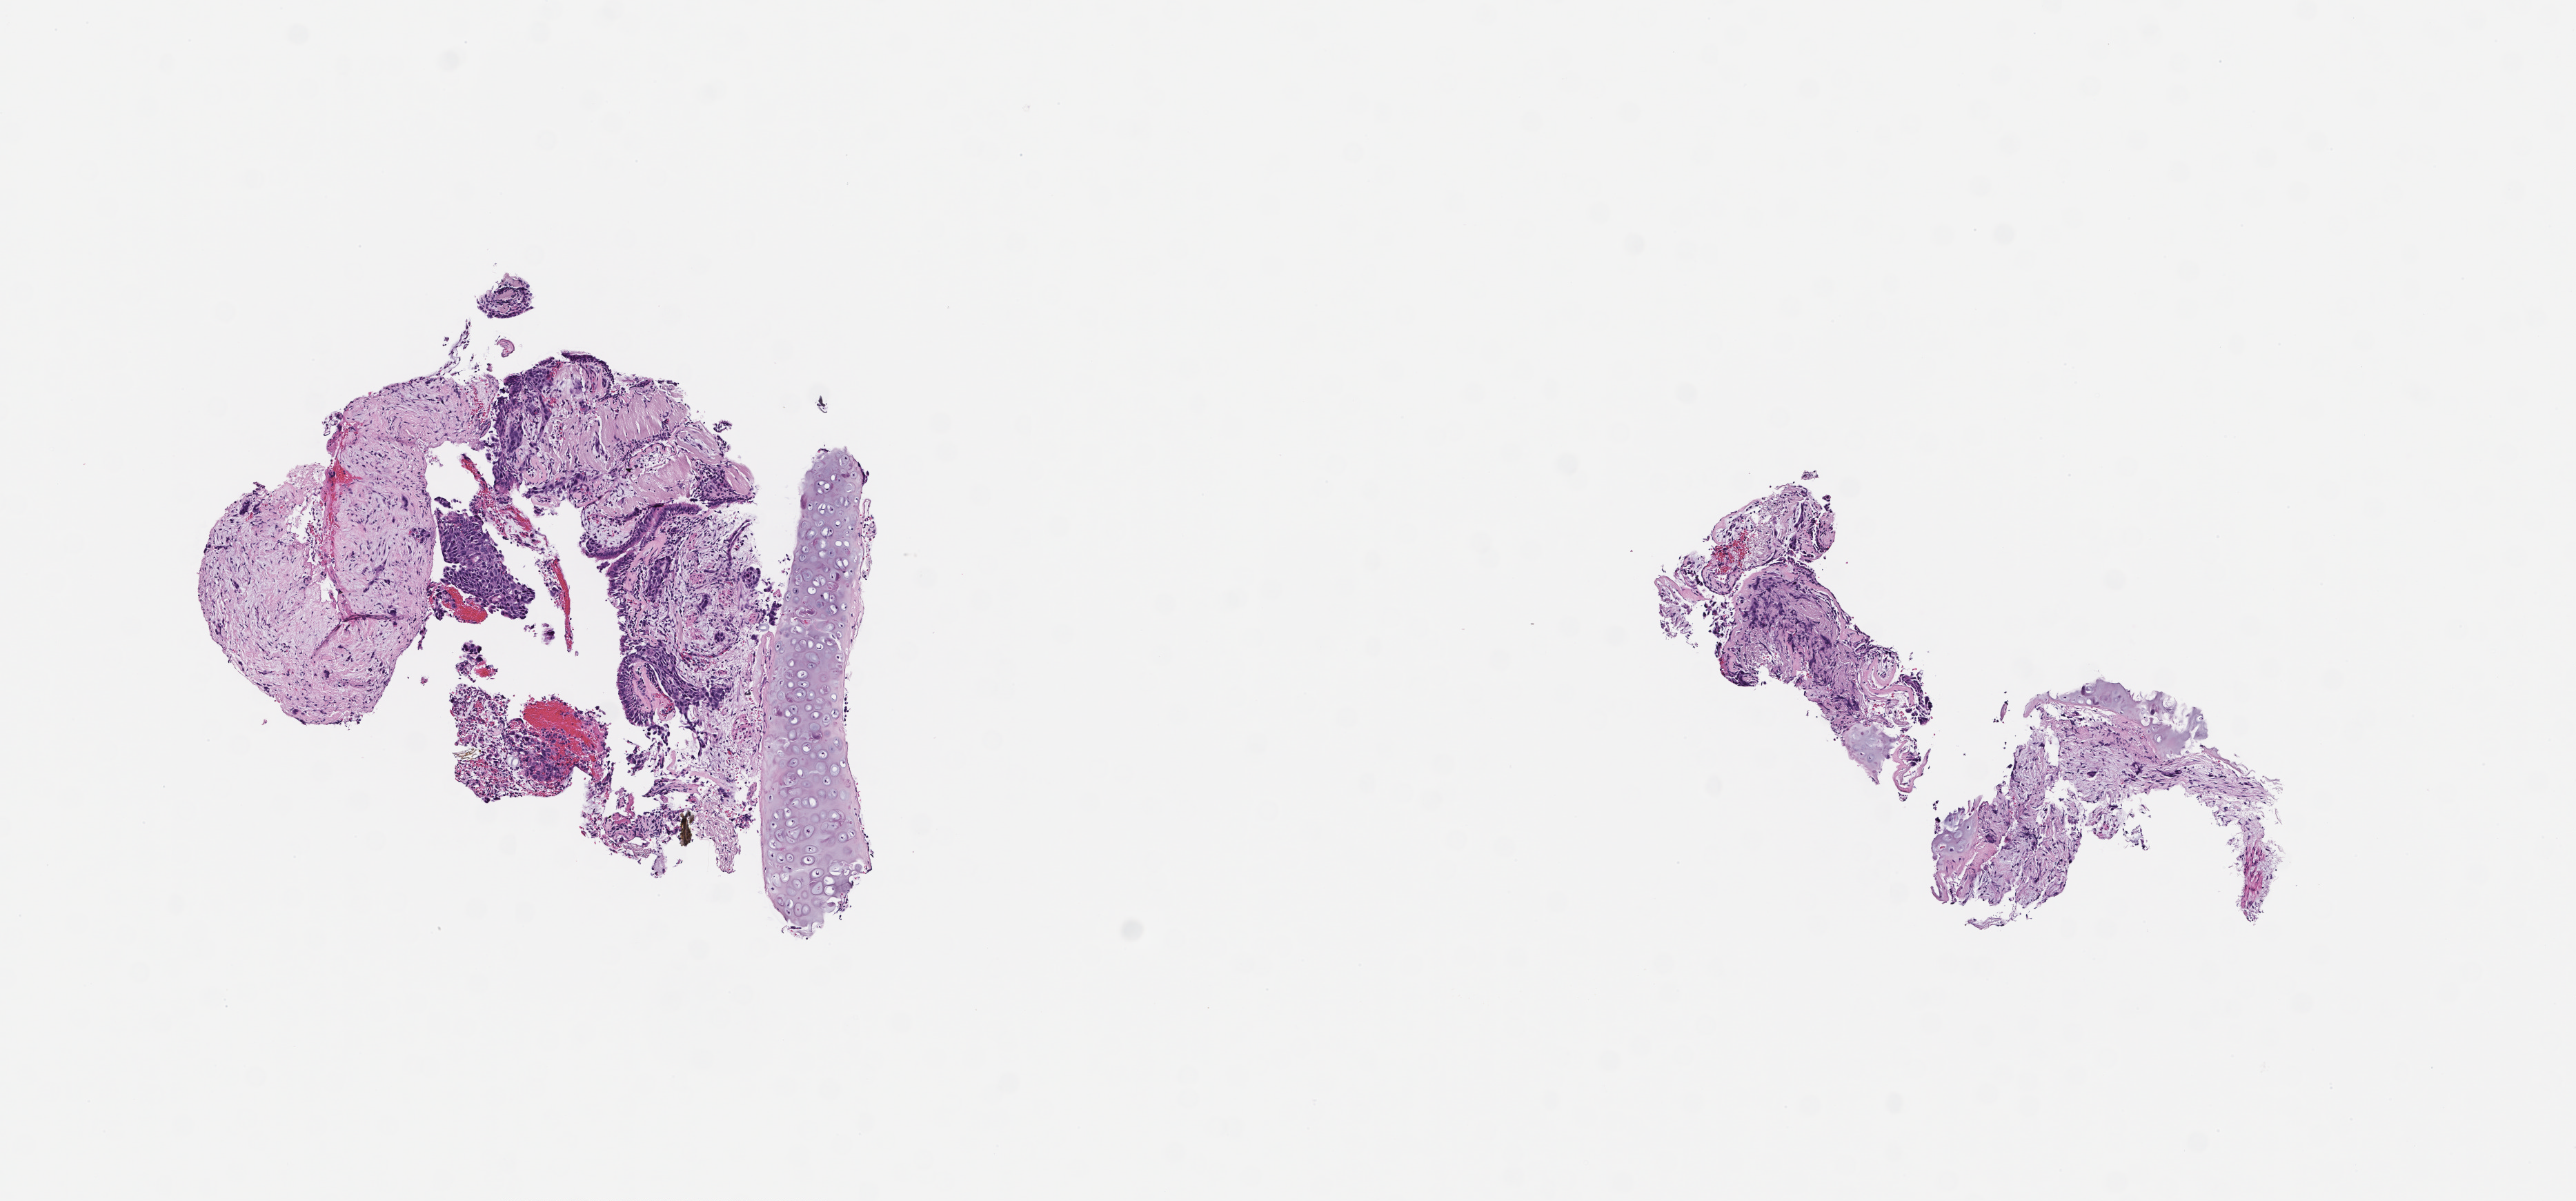
Whole-slide image, haematoxylin and eosin stain, low-resolution overview of the scanned area, about 7.5 x 3.5 mm. FFPE section. Site: lung. Male patient.
• this section: primary tumour tissue
• diagnosis: Non-Small Cell Lung Carcinoma